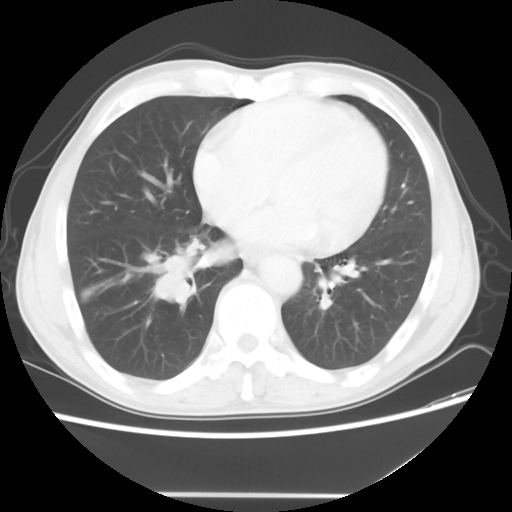
Chest CT, one axial slice; position 20 of 56 along the scan axis; 120 kVp; lung window (W 1500 / L -600 HU); 5 mm slice thickness; 512 × 512 image matrix, field of view 344 × 344 mm. Male patient, age 65 years. Case-level facts recorded for this patient, not image findings: clinical TNM (as recorded): T1c N3 M0; histopathological grade: G3.
Annotated regions visible in this slice (bounding box drawn by a radiologist):
- lung tumour (recorded histology: small cell carcinoma): box from (x=148, y=230) to (x=205, y=312) px